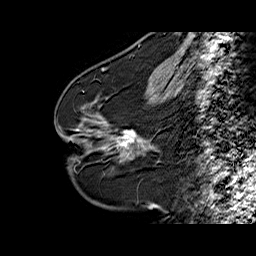
Breast MRI (dynamic contrast-enhanced), one sagittal slice. Position 26 of 60 along the scan axis. Dynamic contrast-enhanced series, time point 2 of 6 at this slice position (early post-contrast). 1.5 T. TE 6.3 ms, TR 32.5 ms. 256 × 256 image matrix. Female patient. Case-level facts recorded for this patient, not image findings: setting: breast cancer imaged before/during neoadjuvant chemotherapy; receptor status: HR-positive, HER2-negative.
Annotated regions visible in this slice (semi-automatically segmented with operator editing):
- analysis volume of interest (the breast-tissue region the enhancement analysis was run in; not a lesion): bounding box [x1, y1, x2, y2] px = [94, 103, 160, 163]
- tumour enhancement mask (voxels above the 100 % enhancement threshold inside the analysis volume of interest): [117, 131, 136, 146]